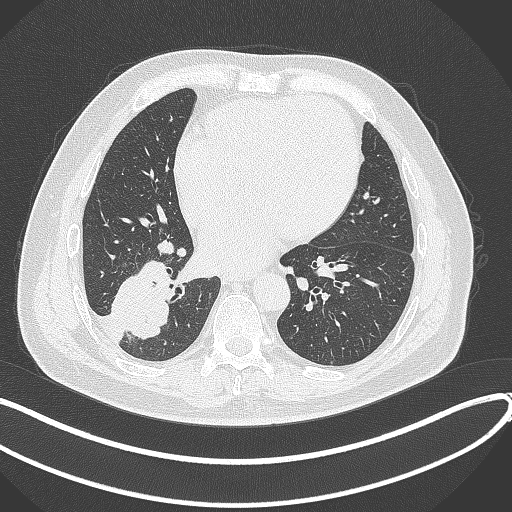
Chest CT, one axial slice. Reconstruction kernel B70f. Lung window (W 1500 / L -600 HU). 1 mm slice thickness. 512 × 512 image matrix. Patient: male, 59 years.
Annotated regions visible in this slice (rectangle marked by the reading radiologist):
- lung tumour (recorded histology: adenocarcinoma): bounding box <108,254,178,342> (left, top, right, bottom; pixels)